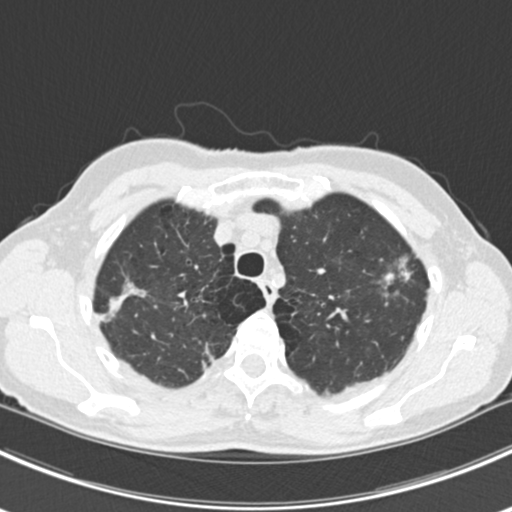
Low-dose screening chest CT, axial slice, first (baseline) screen, lung window (W 1500 / L -600 HU), slice 41 of 224 in the series, 512 × 512 image matrix, field of view 310 × 310 mm. Female participant, aged 63 years at enrolment.
- Lesion marked by an expert reader, bounding box [x1, y1, x2, y2] px = [365, 246, 430, 312].
- The screening reader recorded 10 non-calcified nodules or masses ≥4 mm on this exam; which of them this box marks is not recorded.
- Later outcome: lung cancer diagnosed 751 days after this screen (after the third annual screen) — bronchiolo-alveolar adenocarcinoma, NOS, right upper lobe, right middle lobe, right lower lobe, left upper lobe, left lower lobe, moderately differentiated (G2), stage IV (AJCC 6th edition).